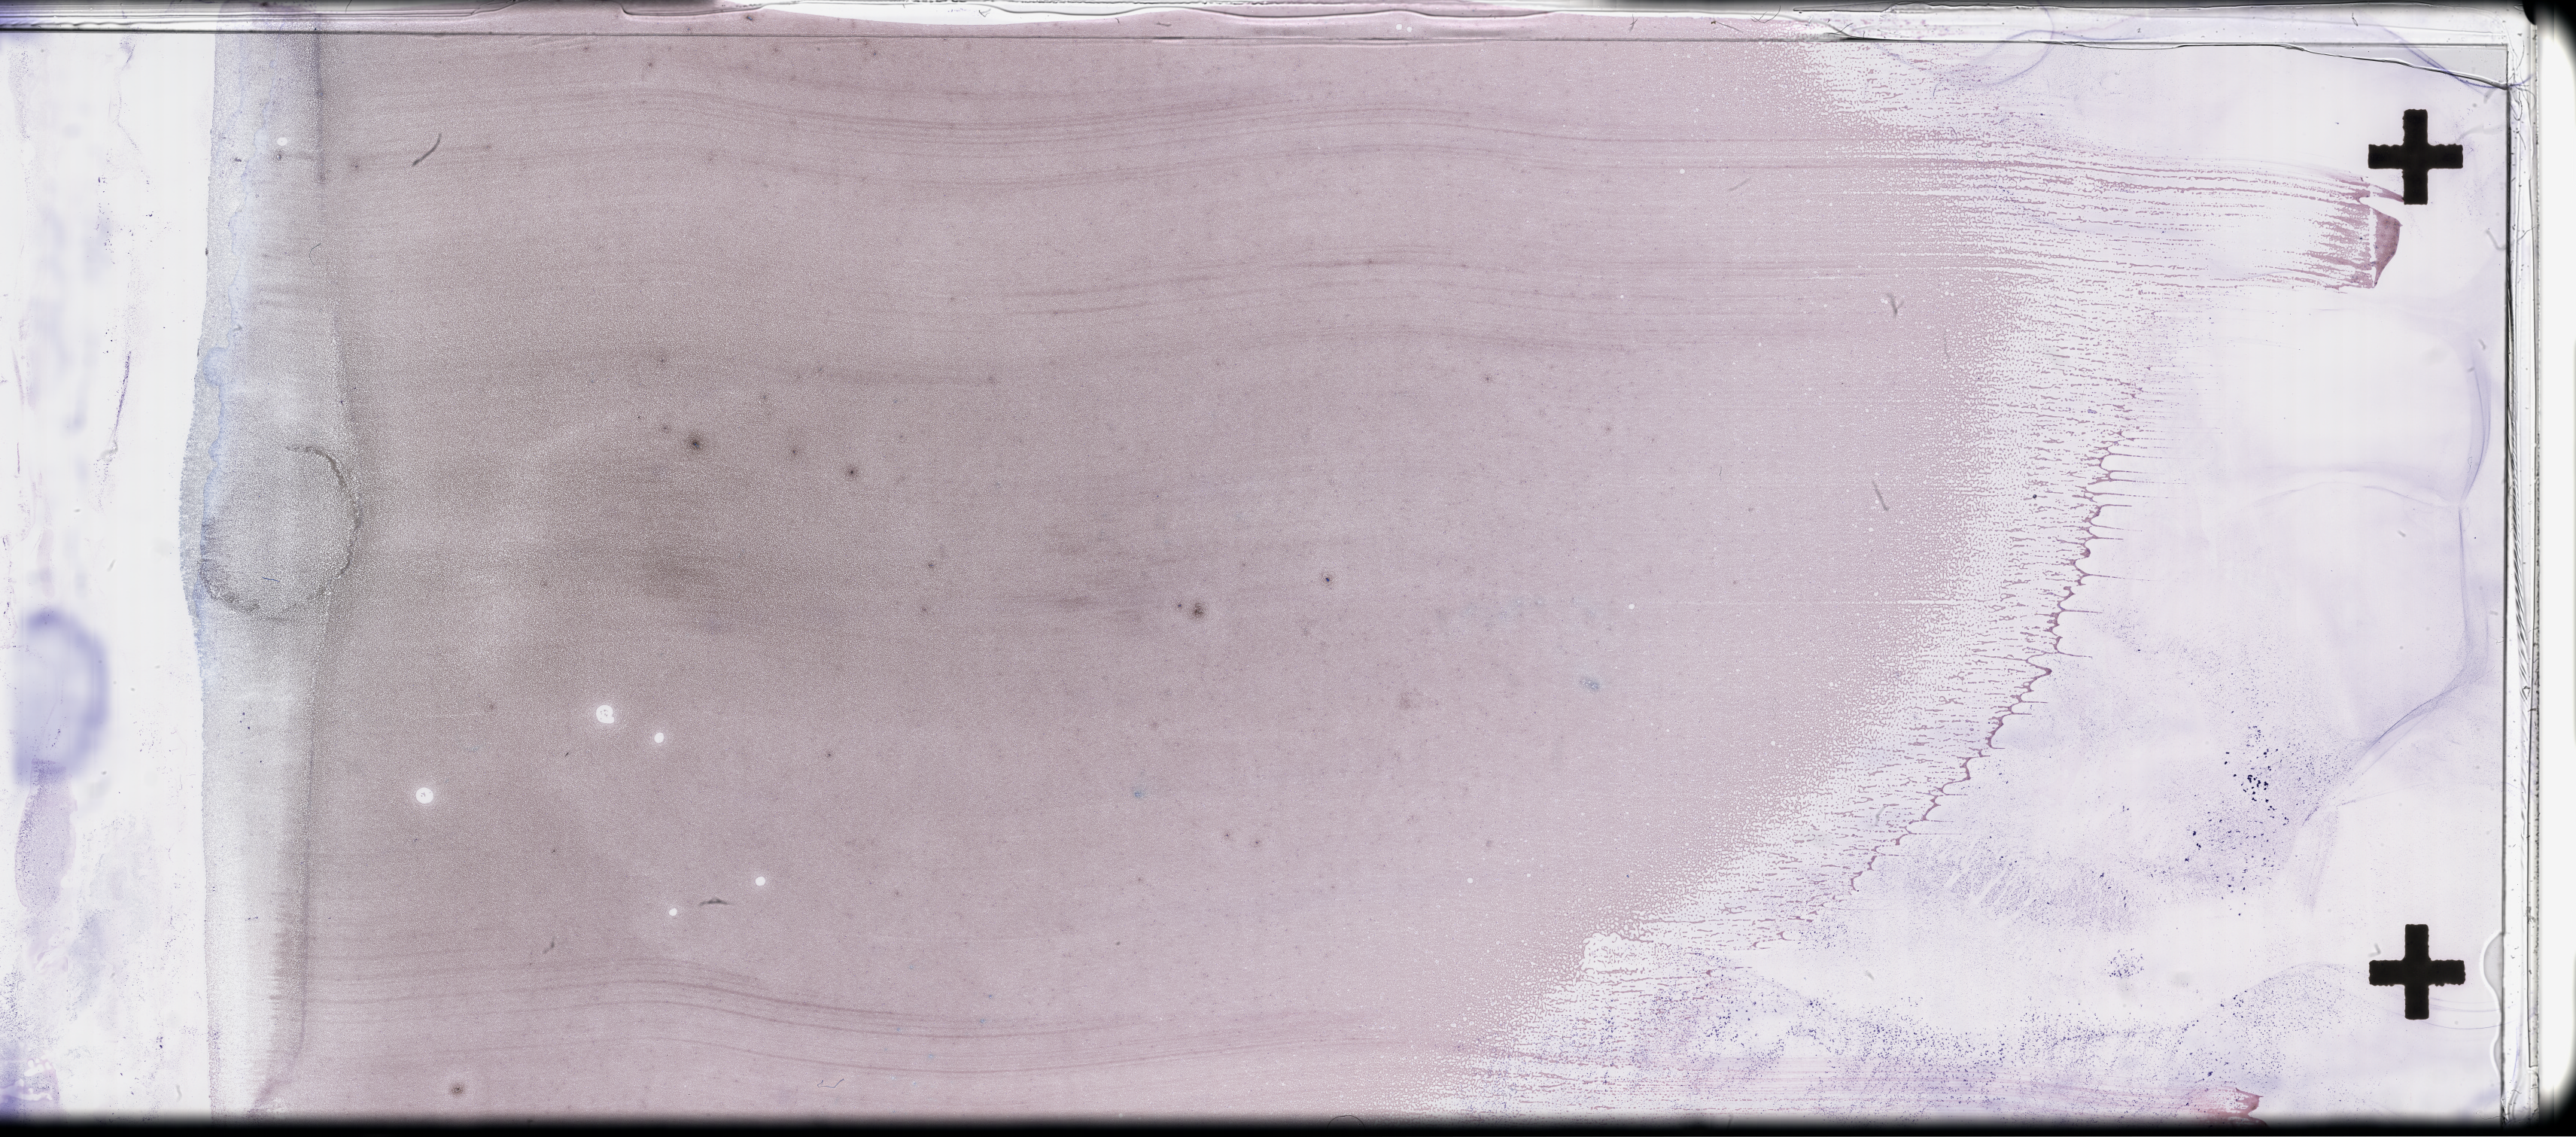
Wright-Giemsa-stained whole blood smear, whole-slide image, low-resolution overview of the scanned area, about 55.3 x 24.4 mm. Male patient.
From a patient with: Plasma Cell Myeloma.